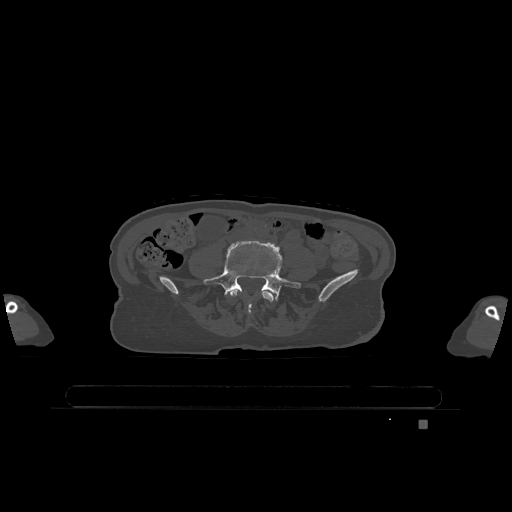
CT including the spine, one axial slice; slice 256 of 1317 in the series (ordered by position); bone window (W 1800 / L 400 HU); 0.5 mm slice thickness; 512 × 512 image matrix, field of view 500 × 500 mm. Female patient, age 74 years. Case-level facts recorded for this patient, not image findings: primary cancer: lung; vertebrae with lytic lesions (as recorded): T1, T4, T5, T6, L4, L5.
Annotated regions visible in this slice (semi-automatically segmented with operator editing):
- L4 vertebra: bounding box <230,290,274,314> (left, top, right, bottom; pixels)
- L5 vertebra: <204,241,301,301>